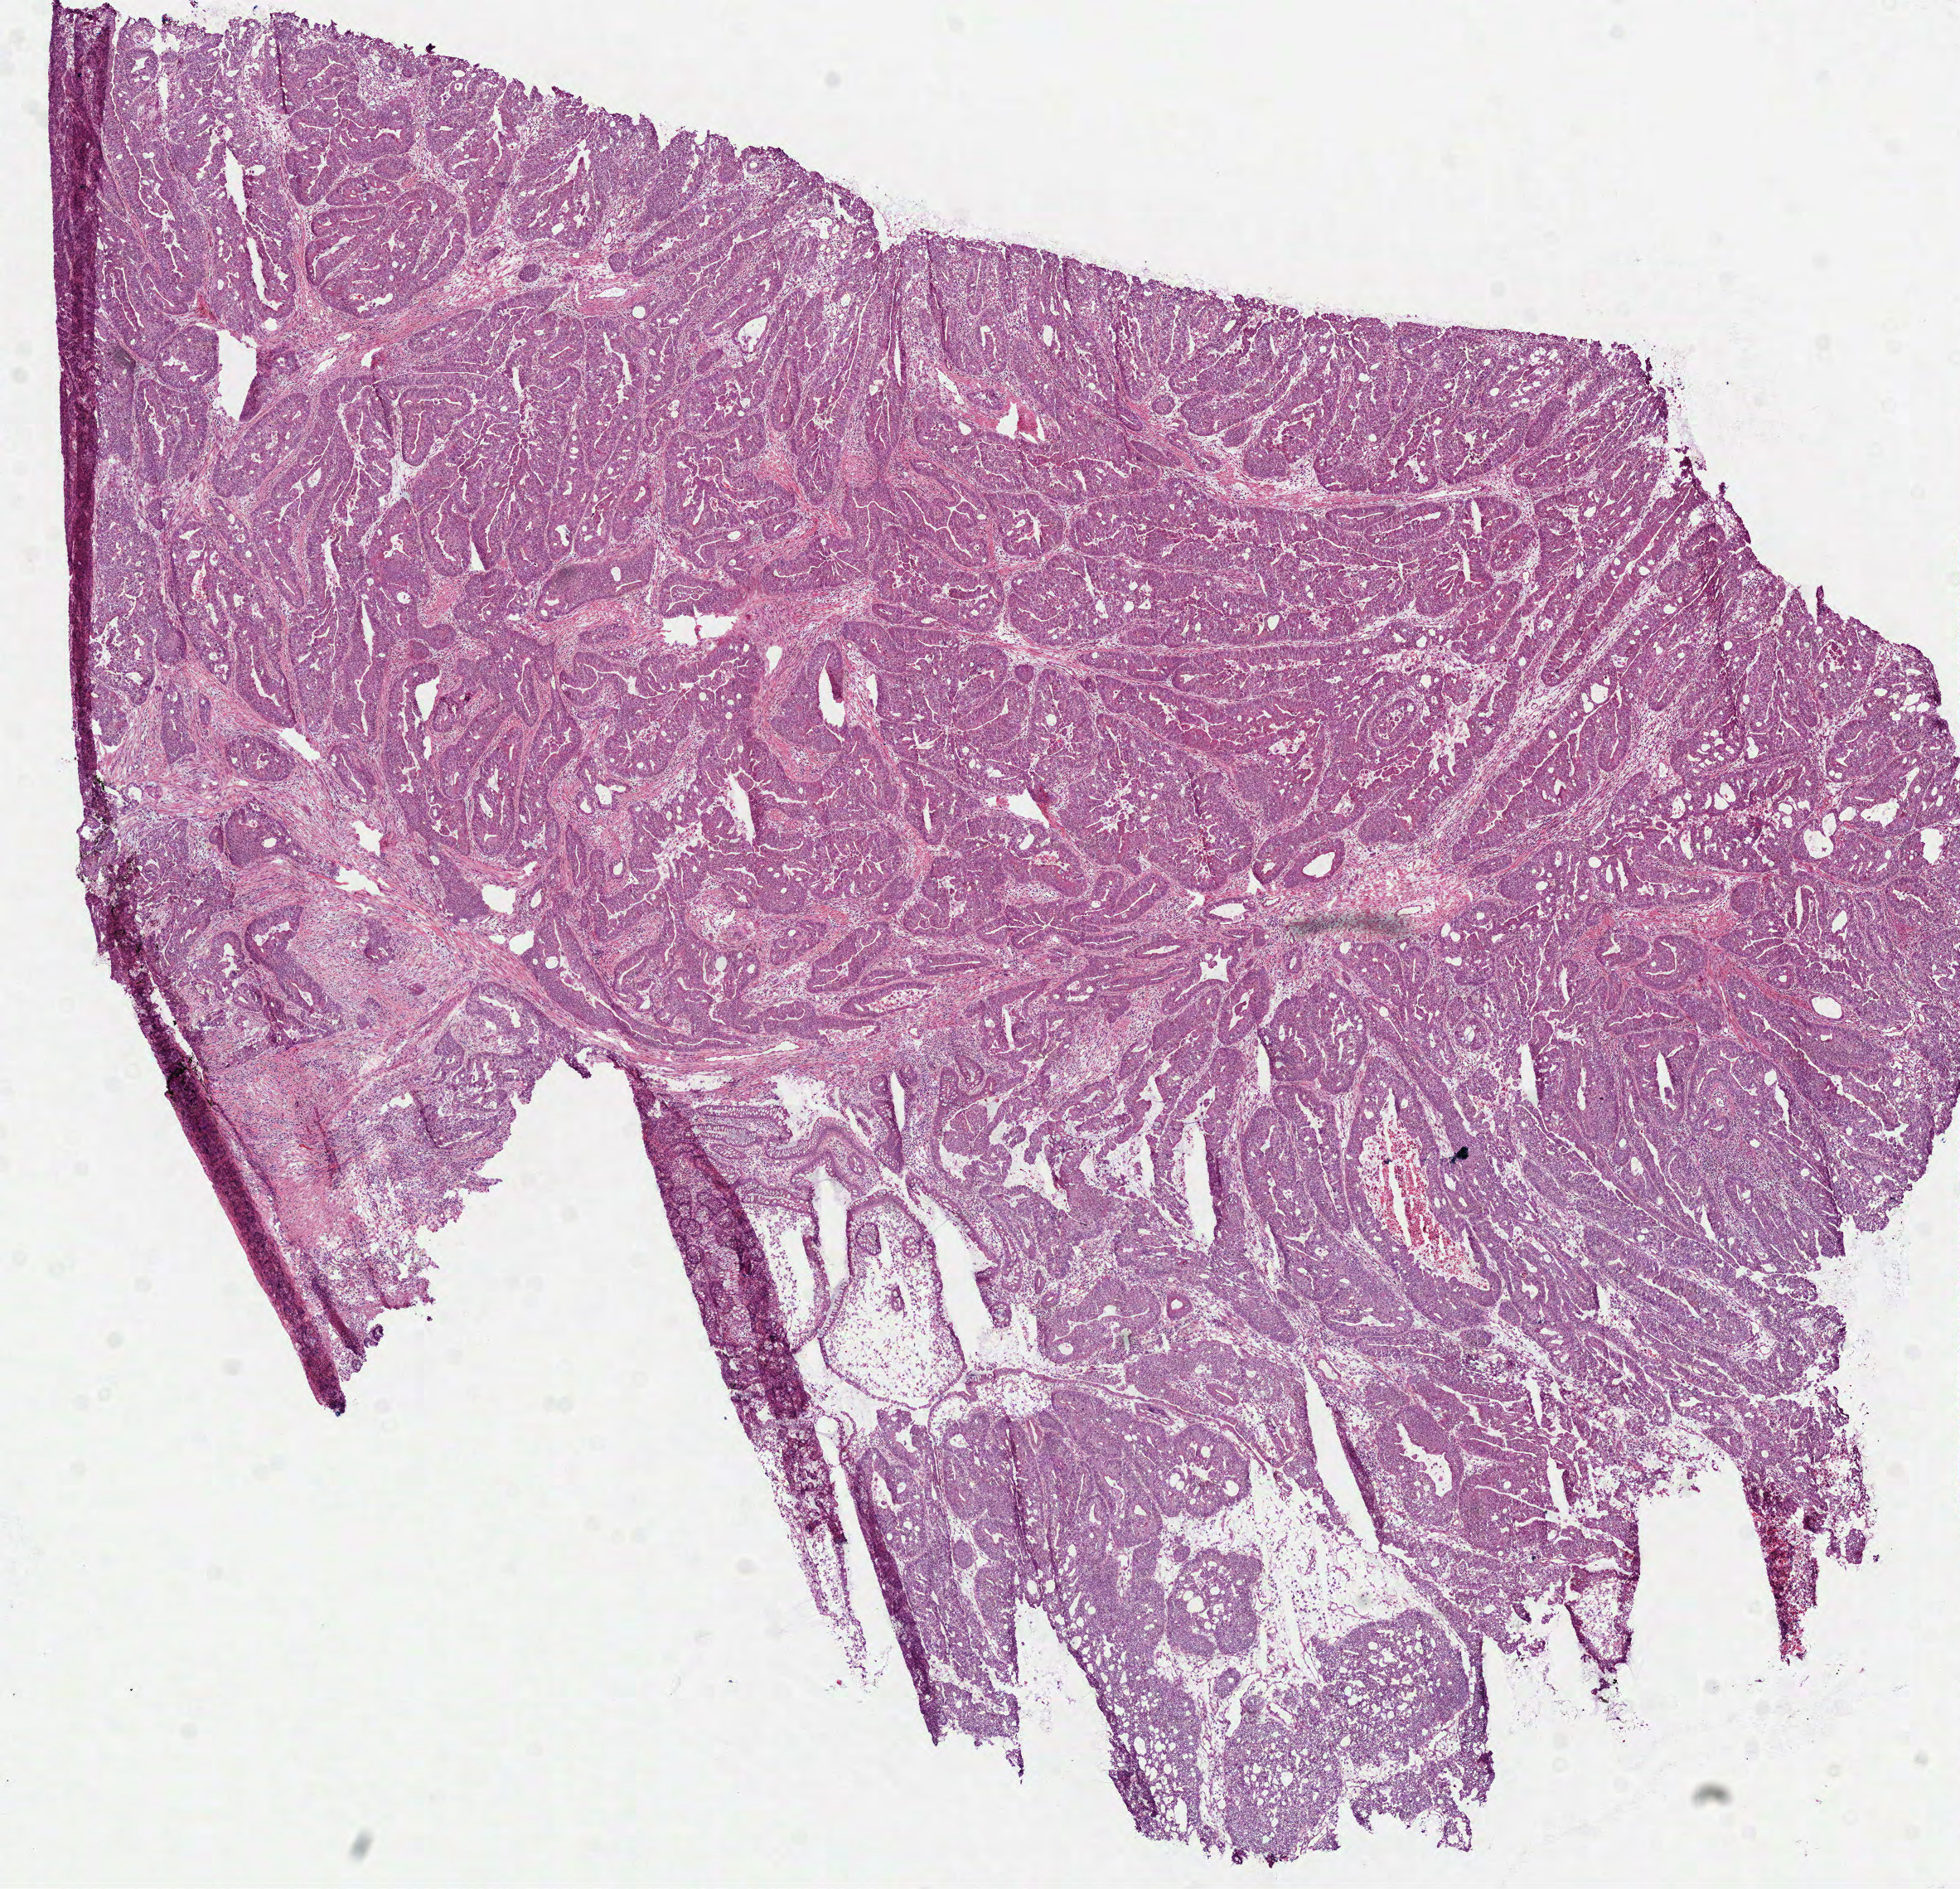
Digitized Hematoxylin and eosin (H&E) stained tissue section (whole slide), low-resolution overview of the scanned area, about 9.5 x 9.2 mm, frozen section from the bottom of the tissue portion, primary tumour sample from the colon. Patient: female, age at initial diagnosis 69 years.
Diagnosis: Adenocarcinoma, NOS (ascending colon).